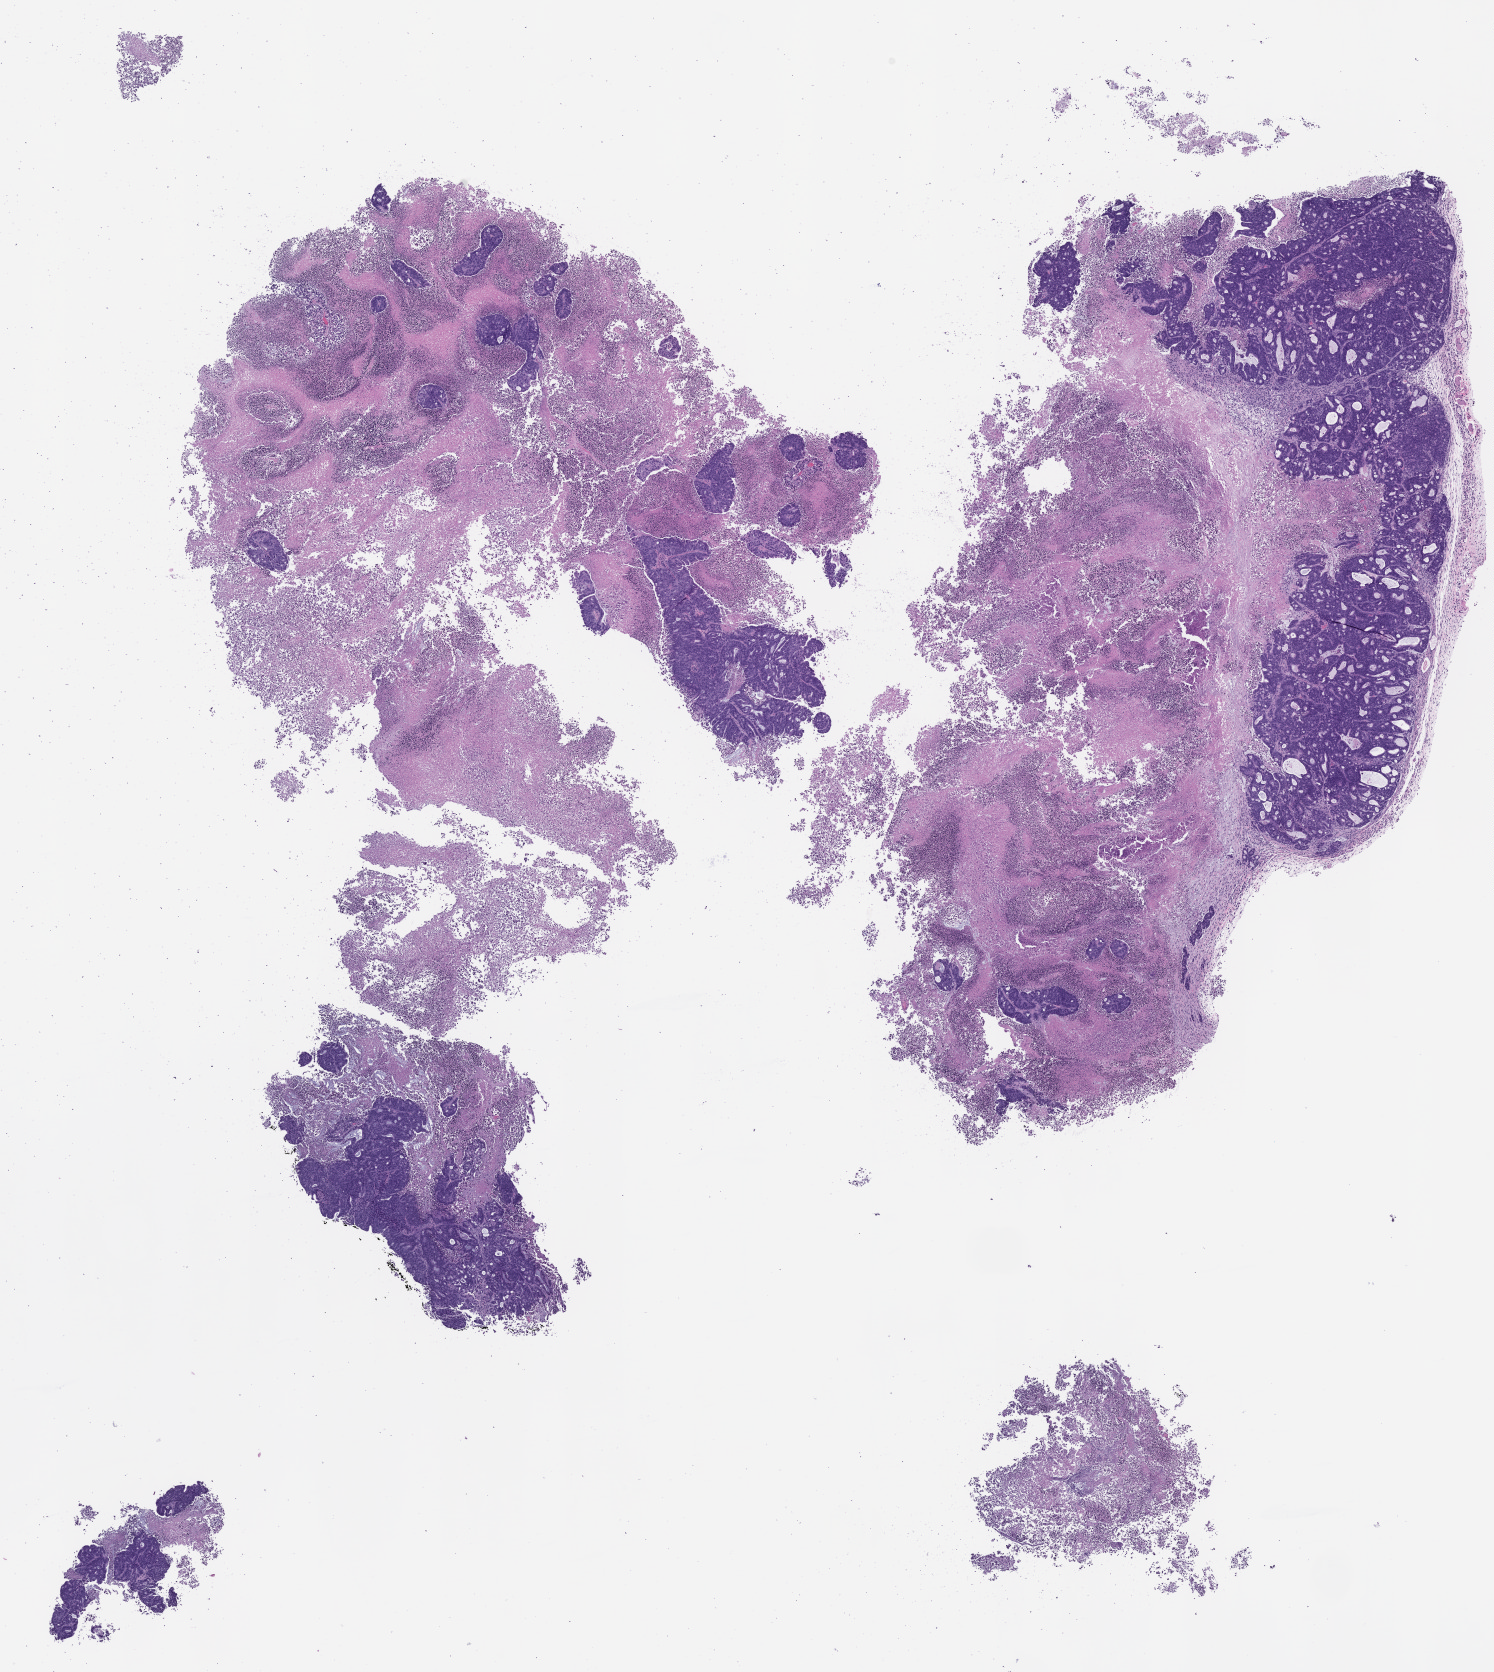
Whole-slide image, haematoxylin and eosin: patient-derived xenograft (human tumor grown in a mouse), passage 1, whole scanned area (about 12.0 x 13.4 mm) shown as a low-resolution overview; formalin-fixed, paraffin-embedded (FFPE) tissue; tumor site category: colon.
* originating patient diagnosis: Colon Adenocarcinoma